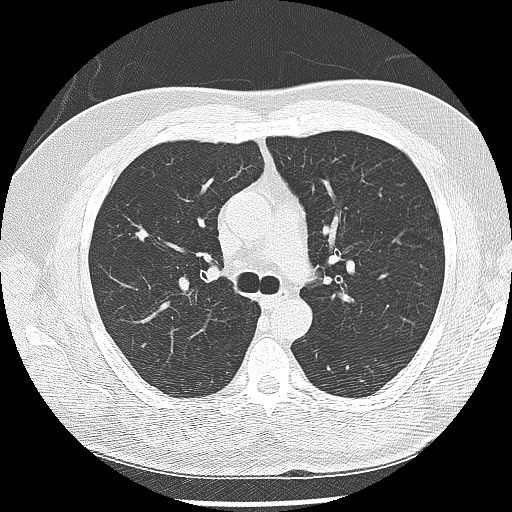
Low-dose screening chest CT, one axial slice. Position 176 of 265 along the scan axis. Reconstruction kernel LUNG. 120 kVp. Lung window (W 1500 / L -600 HU). 512 × 512 image matrix, field of view 340 × 340 mm.
Structures marked on this image (manually delineated by an expert):
- lesion 1 (tumor, upper lobe of right lung): box from (x=135, y=227) to (x=149, y=242) px